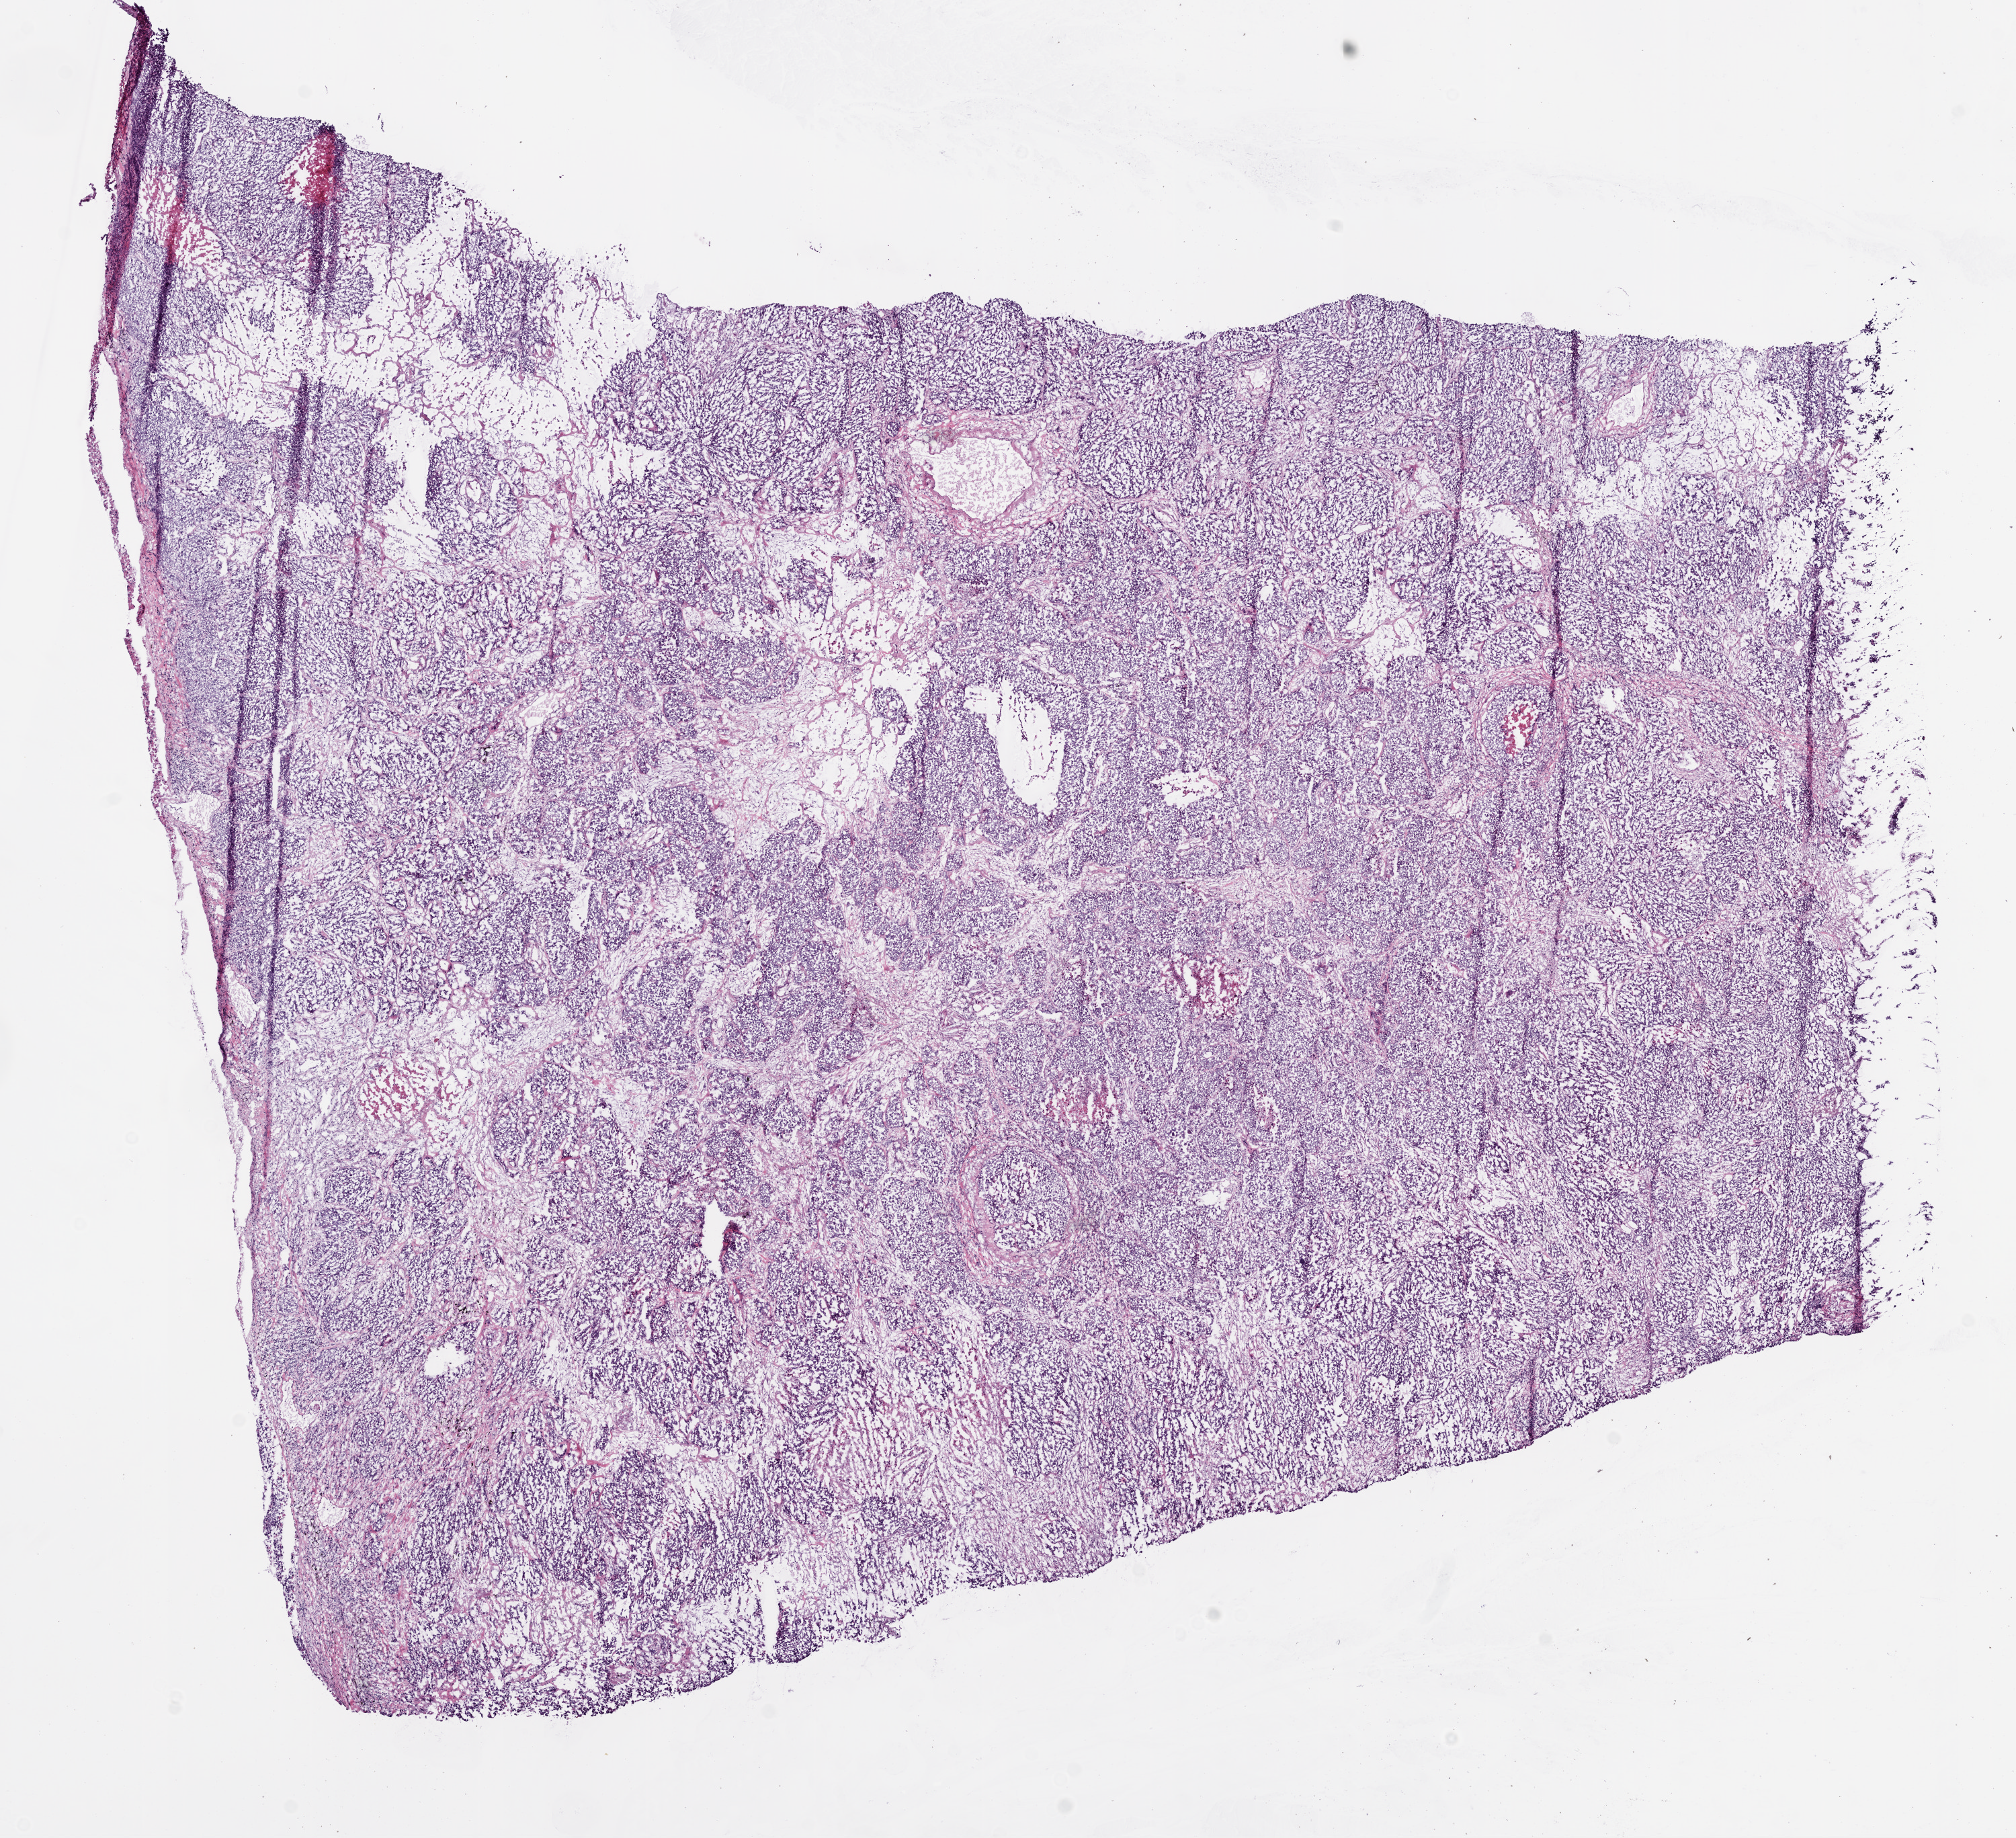
Hematoxylin and eosin (H&E) stained whole-slide image, shown as a low-resolution overview of the whole scanned area (about 12.0 x 11.0 mm, from a 20x scan); frozen section; sample: primary tumour, lung. Male, age 61 years at initial diagnosis. Pathologist review of this section (percent, as recorded): tumour cells 92%, tumour nuclei 75%, normal cells 0%, stromal cells 0%, necrosis 8%. Inflammatory infiltration, as recorded: lymphocyte infiltration 15%, monocyte infiltration 1%, neutrophil infiltration 3%.
• laterality: left
• histologic diagnosis: Adenocarcinoma, NOS (upper lobe, lung)
• AJCC pathologic stage: IIIA